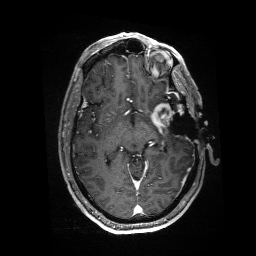
Brain MRI from a brain-tumour surgery series, one axial slice. T1-weighted post-contrast. 256 × 256 image matrix. Case-level facts recorded for this patient, not image findings: histopathology: Glioblastoma; WHO grade: 4; IDH mutation: no; tumour location: Left Anterior/Superior Temporal.
Structures marked on this image (expert manual segmentation):
- residual tumour: bounding box <151,103,184,133> (left, top, right, bottom; pixels)